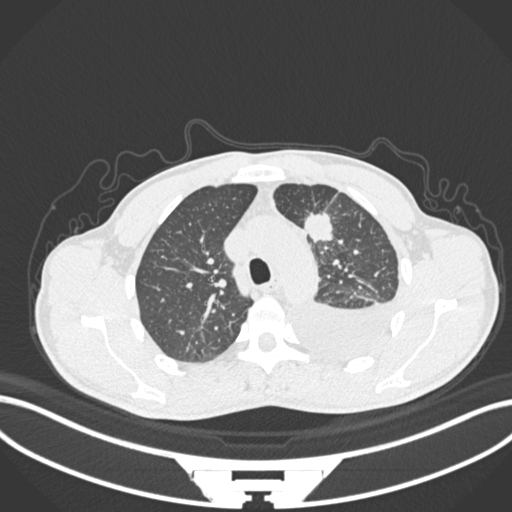
Chest CT, one axial slice; position 162 of 244 along the scan axis; reconstruction kernel B30f; lung window (W 1500 / L -600 HU); 1 mm slice thickness; 512 × 512 image matrix. Male patient, age 49 years. From the clinical record (not read from this slice): clinical TNM (as recorded): T1c N1 M1.
Structures marked on this image (rectangle marked by the reading radiologist):
- lung tumour (recorded histology: adenocarcinoma): bounding box <305,212,335,243> (left, top, right, bottom; pixels)